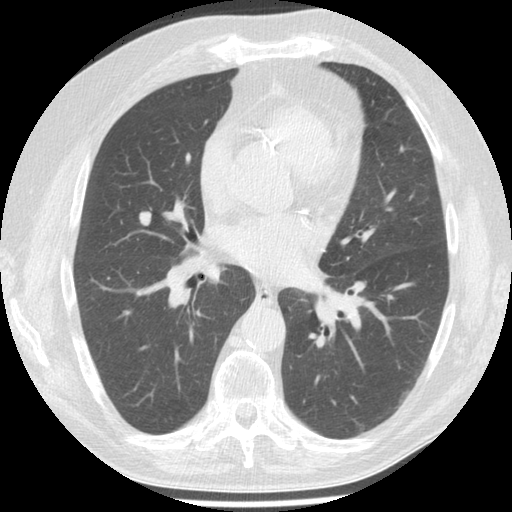
Low-dose screening chest CT, one axial slice. Position 72 of 149 along the scan axis. 120 kVp. Lung window (W 1500 / L -600 HU). 2.5 mm slice thickness. 512 × 512 image matrix, field of view 340 × 340 mm.
Structures marked on this image (expert manual segmentation):
- lesion 1 (tumor, middle lobe of right lung): bounding box [x1, y1, x2, y2] px = [139, 211, 152, 226]